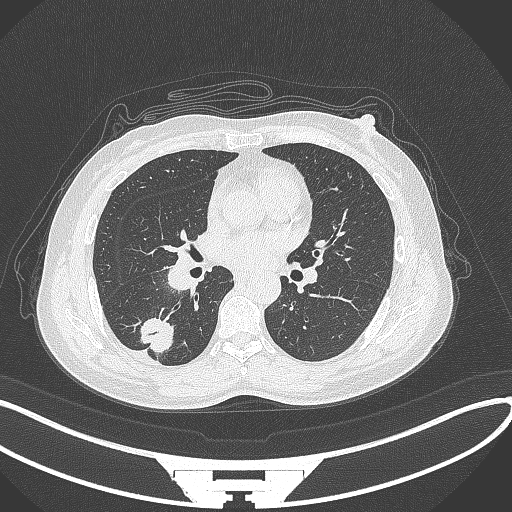
Chest CT, one axial slice; position 151 of 352 along the scan axis; reconstruction kernel B70f; 120 kVp; lung window (W 1500 / L -600 HU); 512 × 512 image matrix. Female patient, age 55 years. From the clinical record (not read from this slice): clinical TNM (as recorded): T1c N1 M0.
Annotated regions visible in this slice (bounding box drawn by a radiologist):
- lung tumour (recorded histology: adenocarcinoma): bounding box [x1, y1, x2, y2] px = [137, 314, 178, 357]